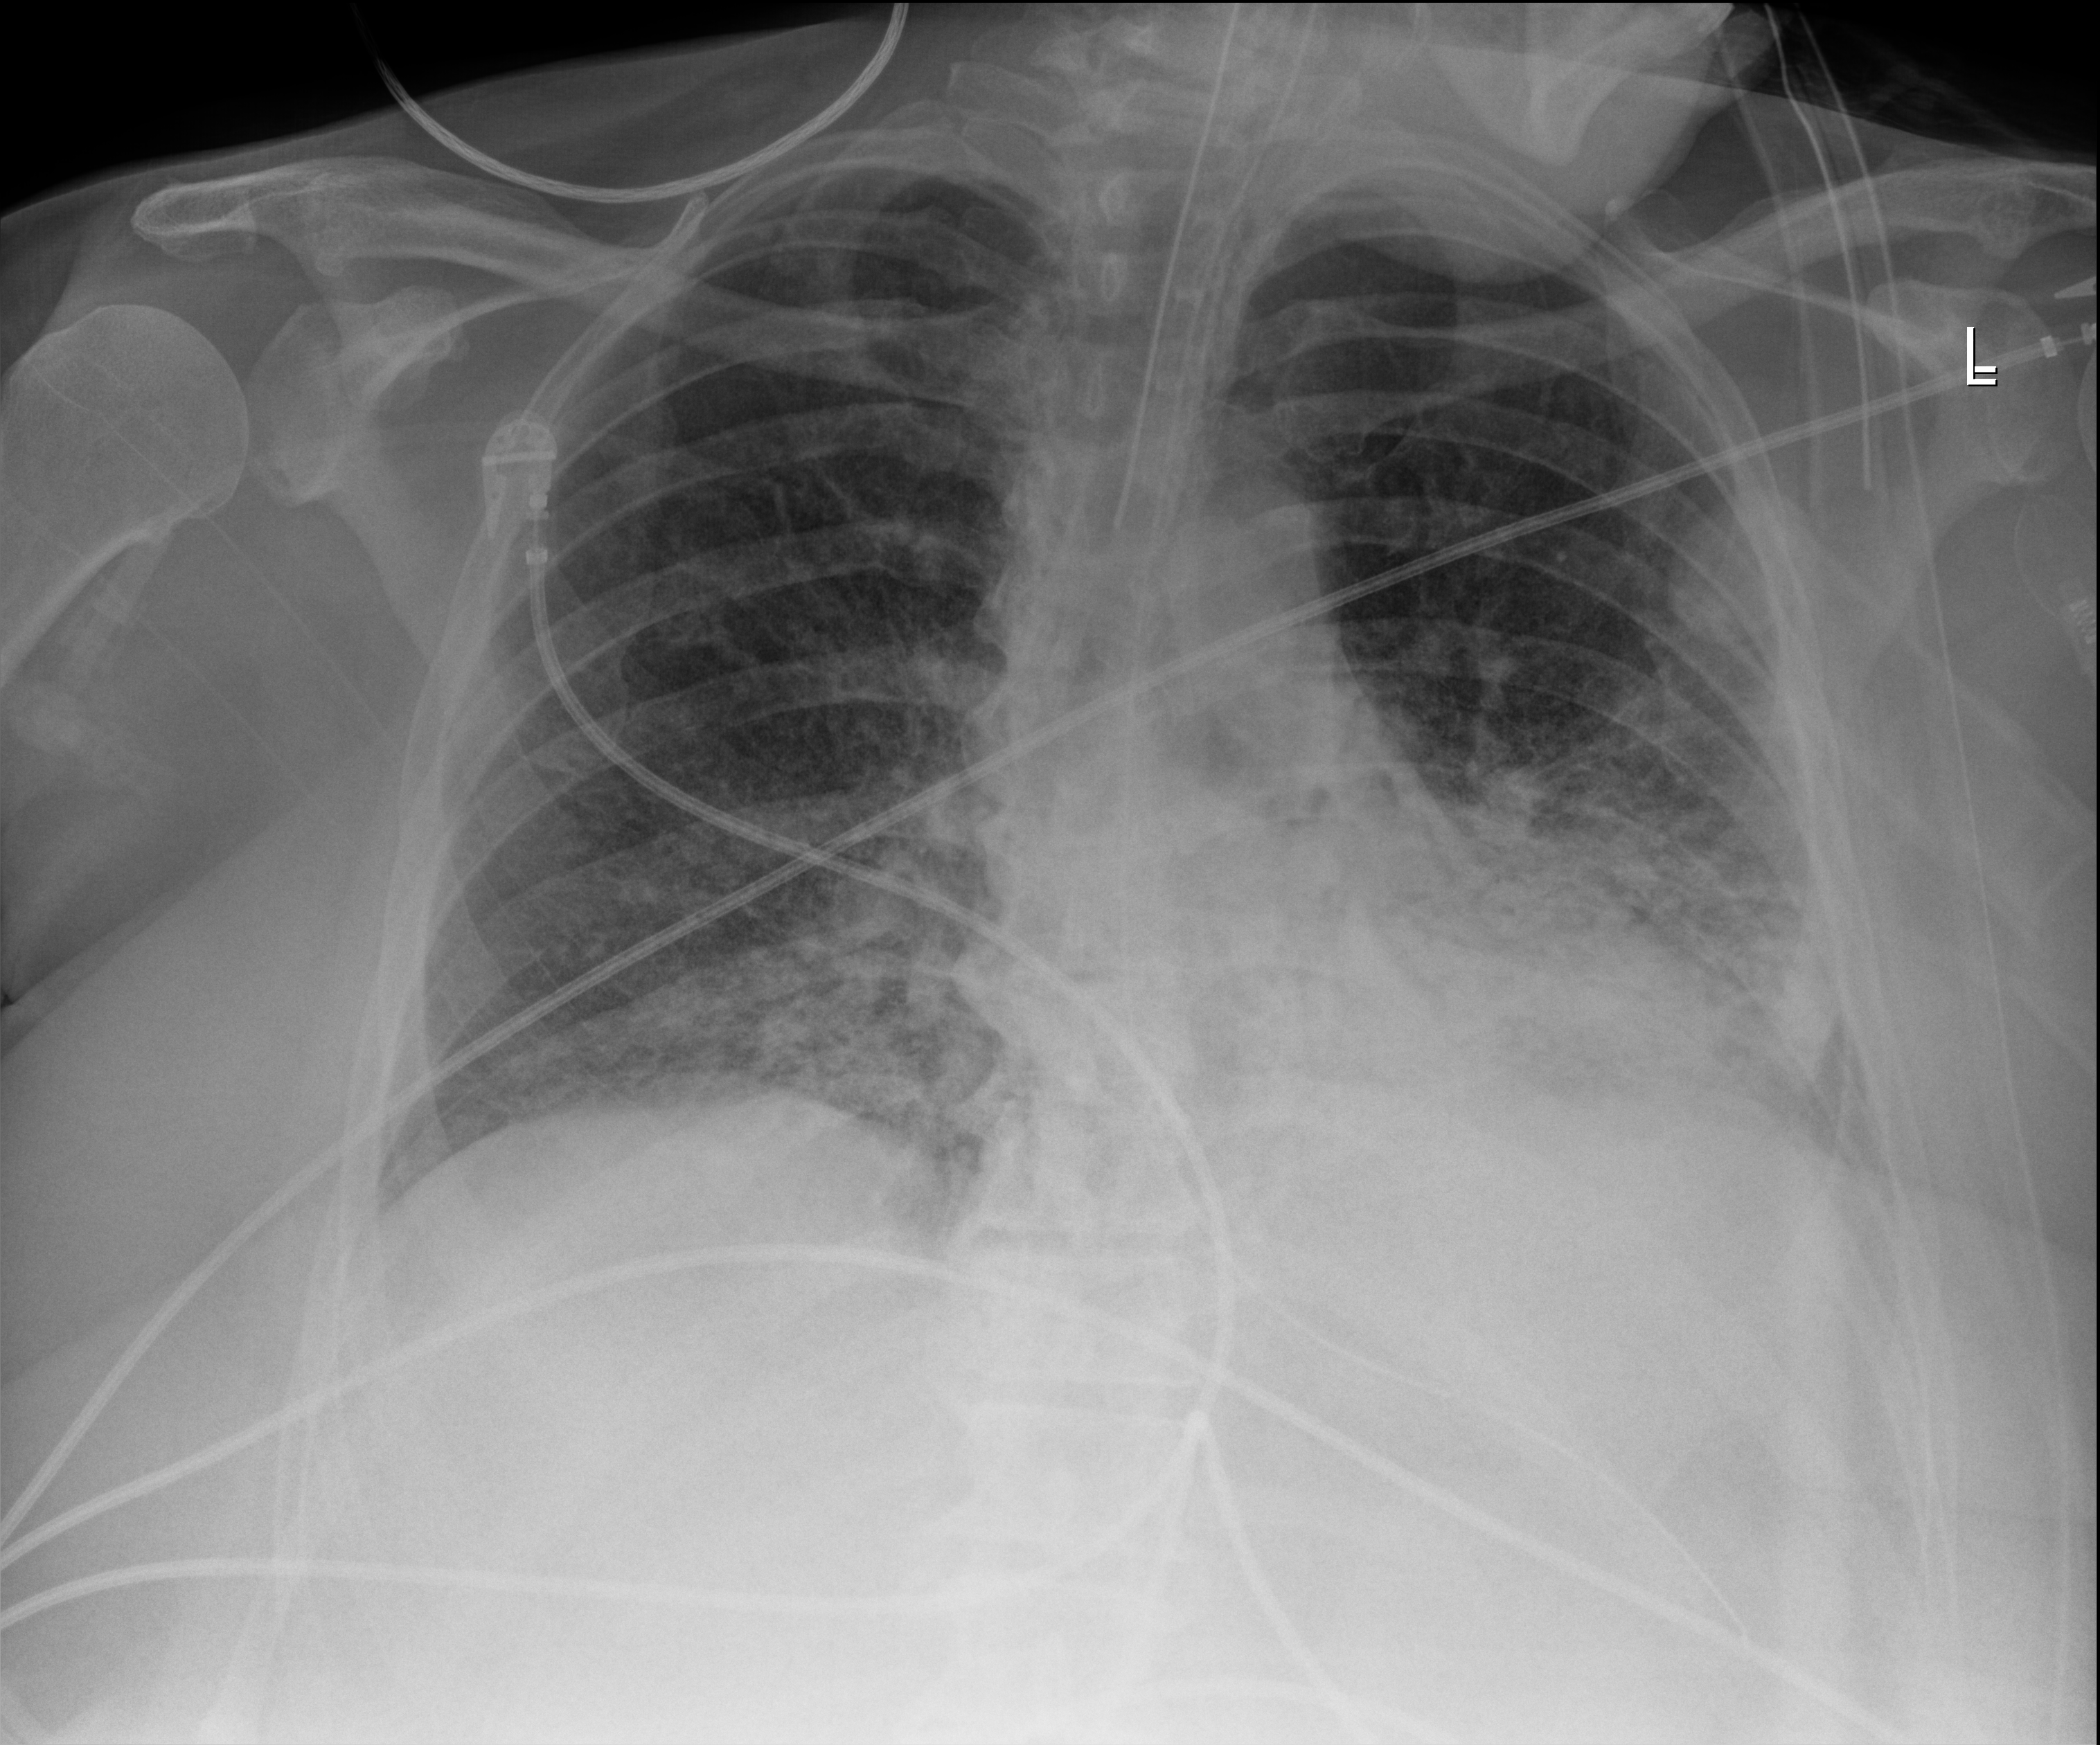
Chest X-ray; anteroposterior (AP) projection. Patient hospitalised with COVID-19, aged 18–59 years.
From the hospital-stay record, not from the radiograph (when in the stay this image was taken is not recorded): admitted to intensive care during this hospital stay: yes; mechanically ventilated during this hospital stay: yes.